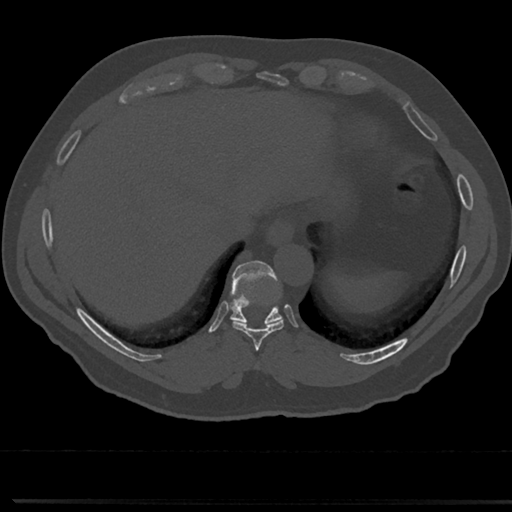
CT including the spine, one axial slice; slice 286 of 817 in the series (ordered by position); 120 kVp; bone window (W 1800 / L 400 HU); 512 × 512 image matrix, field of view 355 × 355 mm. Male patient, age 61 years. From the clinical record (not read from this slice): primary cancer: prostate.
Structures marked on this image (semi-automatically segmented with operator editing):
- T8 vertebra: bounding box <255,352,263,372> (left, top, right, bottom; pixels)
- T9 vertebra: <211,263,304,351>